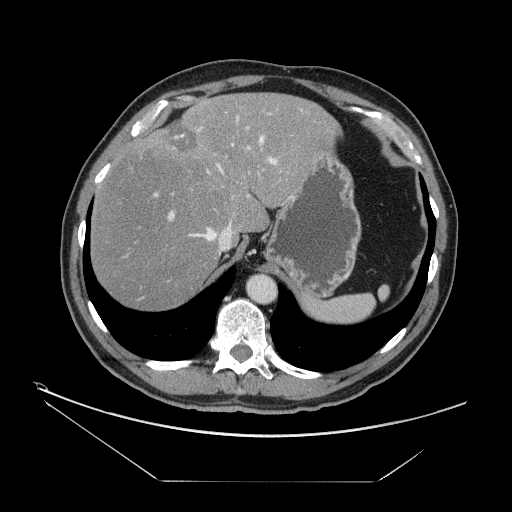
Contrast-enhanced abdominal CT, one axial slice. Position 119 of 161 along the scan axis. Reconstruction kernel STANDARD. Intravenous contrast given. Soft-tissue window (W 400 / L 40 HU). 2.5 mm slice thickness. 512 × 512 image matrix. Male patient, age 65 years. Case-level facts recorded for this patient, not image findings: diagnosis: colorectal cancer liver metastases, imaged before liver resection; multiple liver metastases: yes; largest metastasis: 4.2 cm.
Structures marked on this image (expert manual segmentation):
- hepatic veins: bounding box <188,136,264,254> (left, top, right, bottom; pixels)
- liver: <90,93,336,312>
- planned liver remnant (the part of the liver to remain after resection): <90,93,336,312>
- portal vein (with intrahepatic branches): <154,109,306,221>
- liver metastasis: <166,120,197,154>